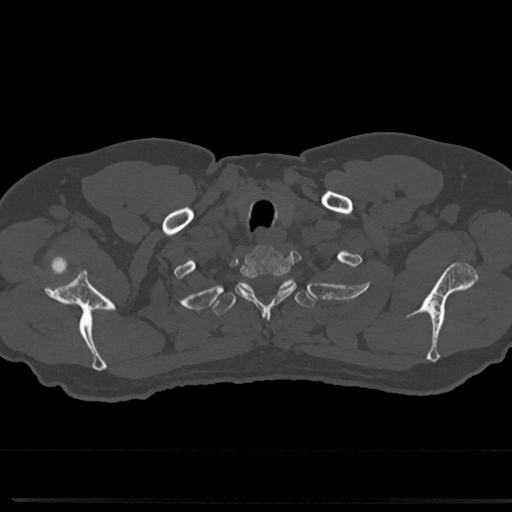
CT including the spine, one axial slice; reconstruction kernel Br40s/3; bone window (W 1800 / L 400 HU); 0.5 mm slice thickness; 512 × 512 image matrix, field of view 355 × 355 mm. Patient: male, 61 years. From the clinical record (not read from this slice): primary cancer: prostate.
Outlined on this slice (semi-automatic segmentation, software-assisted and operator-edited):
- T1 vertebra: bounding box <237,248,294,302> (left, top, right, bottom; pixels)
- T2 vertebra: <215,278,313,314>